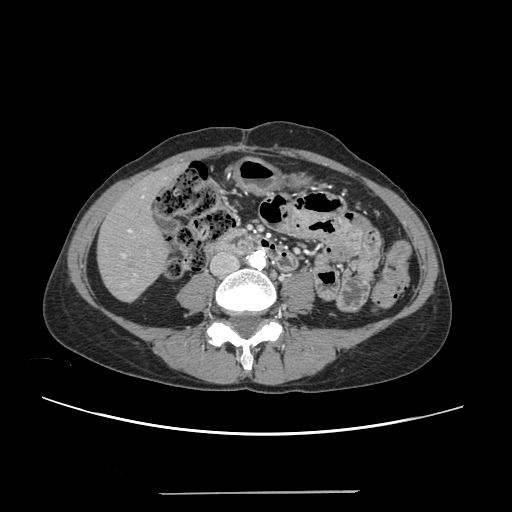
Contrast-enhanced abdominal CT, one axial slice; slice 56 of 240 in the series (ordered by position); 120 kVp; intravenous contrast given; soft-tissue window (W 400 / L 40 HU); 1.25 mm slice thickness; 512 × 512 image matrix. Female patient, age 60 years. From the clinical record (not read from this slice): diagnosis: colorectal cancer liver metastases, imaged before liver resection; multiple liver metastases: no; largest metastasis: 1.5 cm; disease in both lobes: no.
Outlined on this slice (manually delineated by an expert):
- liver: box from (x=98, y=168) to (x=179, y=301) px
- planned liver remnant (the part of the liver to remain after resection): (x=98, y=171)–(x=171, y=301)
- portal vein (with intrahepatic branches): (x=122, y=187)–(x=146, y=278)